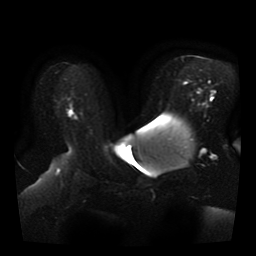
Breast MRI, one axial slice. Slice 23 of 41 in the series (ordered by position). Diffusion-weighted series; image 2 of 4 stored at this slice position (different b-values; order by instance number). 1.5 T. 5 mm slice thickness. 256 × 256 image matrix. Female patient.
Outlined on this slice (manually delineated by an expert):
- tumour on diffusion-weighted imaging: bounding box <69,110,73,117> (left, top, right, bottom; pixels)